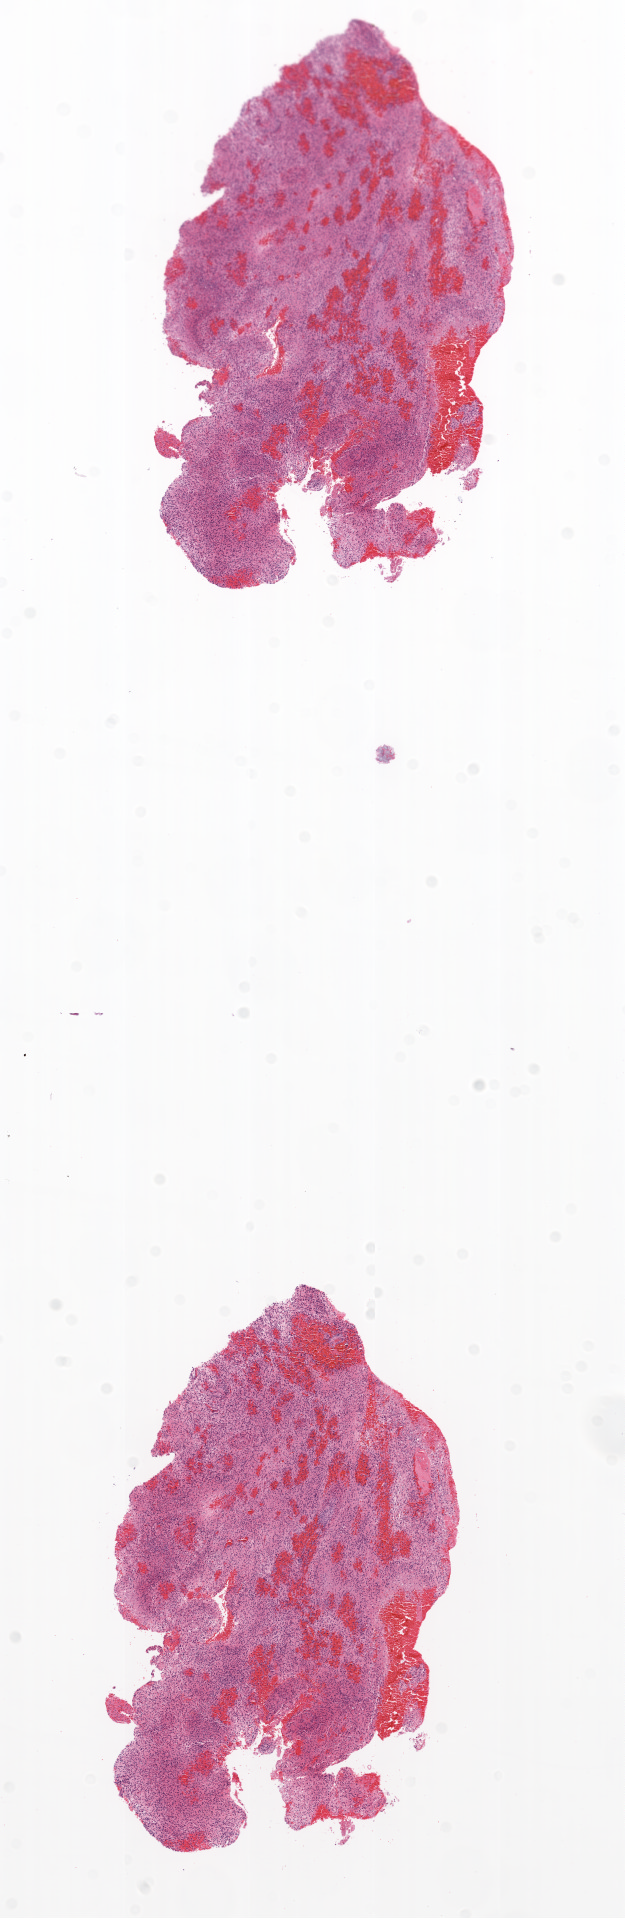
H&E whole-slide image — low-resolution overview of the scanned area, about 5.0 x 15.4 mm (from a 20x scan), formalin-fixed paraffin-embedded (FFPE) diagnostic section, primary tumour sample from the brain. Male, age 43 years at initial diagnosis.
Diagnosis: Glioblastoma.